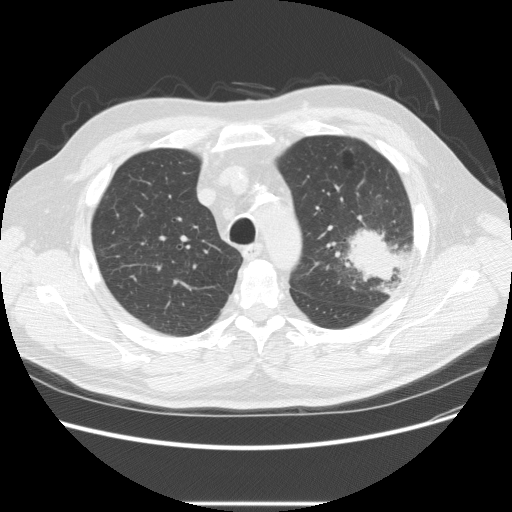
Low-dose screening chest CT, one axial slice. Slice 174 of 233 in the series (ordered by position). Reconstruction kernel STANDARD. 120 kVp. Lung window (W 1500 / L -600 HU). 2.5 mm slice thickness. 512 × 512 image matrix.
Annotated regions visible in this slice (expert manual segmentation):
- lesion 1 (tumor, upper lobe of left lung): box from (x=345, y=226) to (x=401, y=285) px